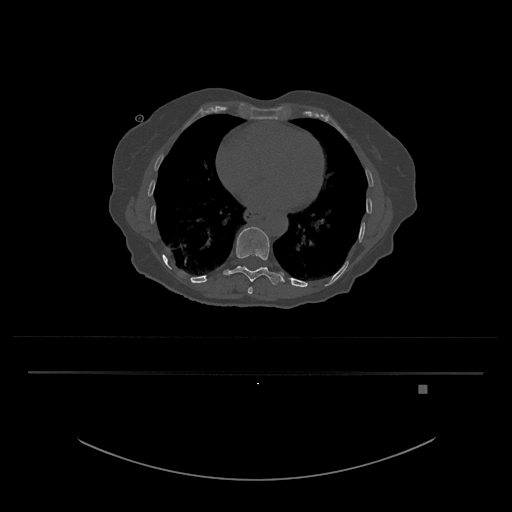
CT including the spine, one axial slice; position 713 of 797 along the scan axis; reconstruction kernel Br40s/3; bone window (W 1800 / L 400 HU); 0.5 mm slice thickness; 512 × 512 image matrix, field of view 500 × 500 mm. Female patient, age 57 years. Case-level facts recorded for this patient, not image findings: primary cancer: cervical.
Outlined on this slice (semi-automatically segmented with operator editing):
- T10 vertebra: box from (x=224, y=227) to (x=285, y=285) px
- T9 vertebra: (x=247, y=287)–(x=253, y=294)